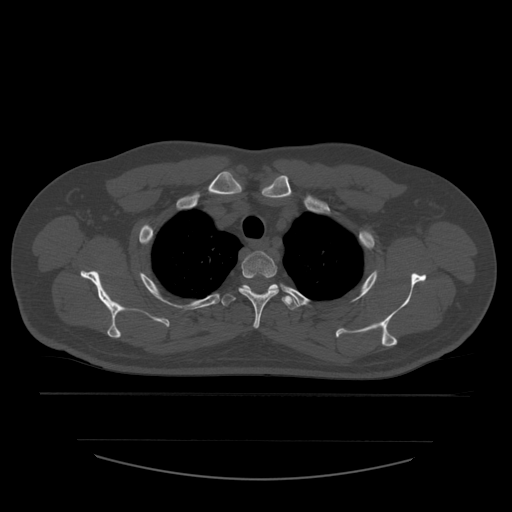
CT including the spine, one axial slice; slice 446 of 532 in the series (ordered by position); 120 kVp; bone window (W 1800 / L 400 HU); 512 × 512 image matrix. Patient age 44 years. Case-level facts recorded for this patient, not image findings: primary cancer: soft tissue sarcoma.
Structures marked on this image (semi-automatic segmentation, software-assisted and operator-edited):
- T2 vertebra: bounding box (x1, y1, x2, y2) in pixels: (239, 251, 280, 329)
- T3 vertebra: (221, 284, 299, 311)